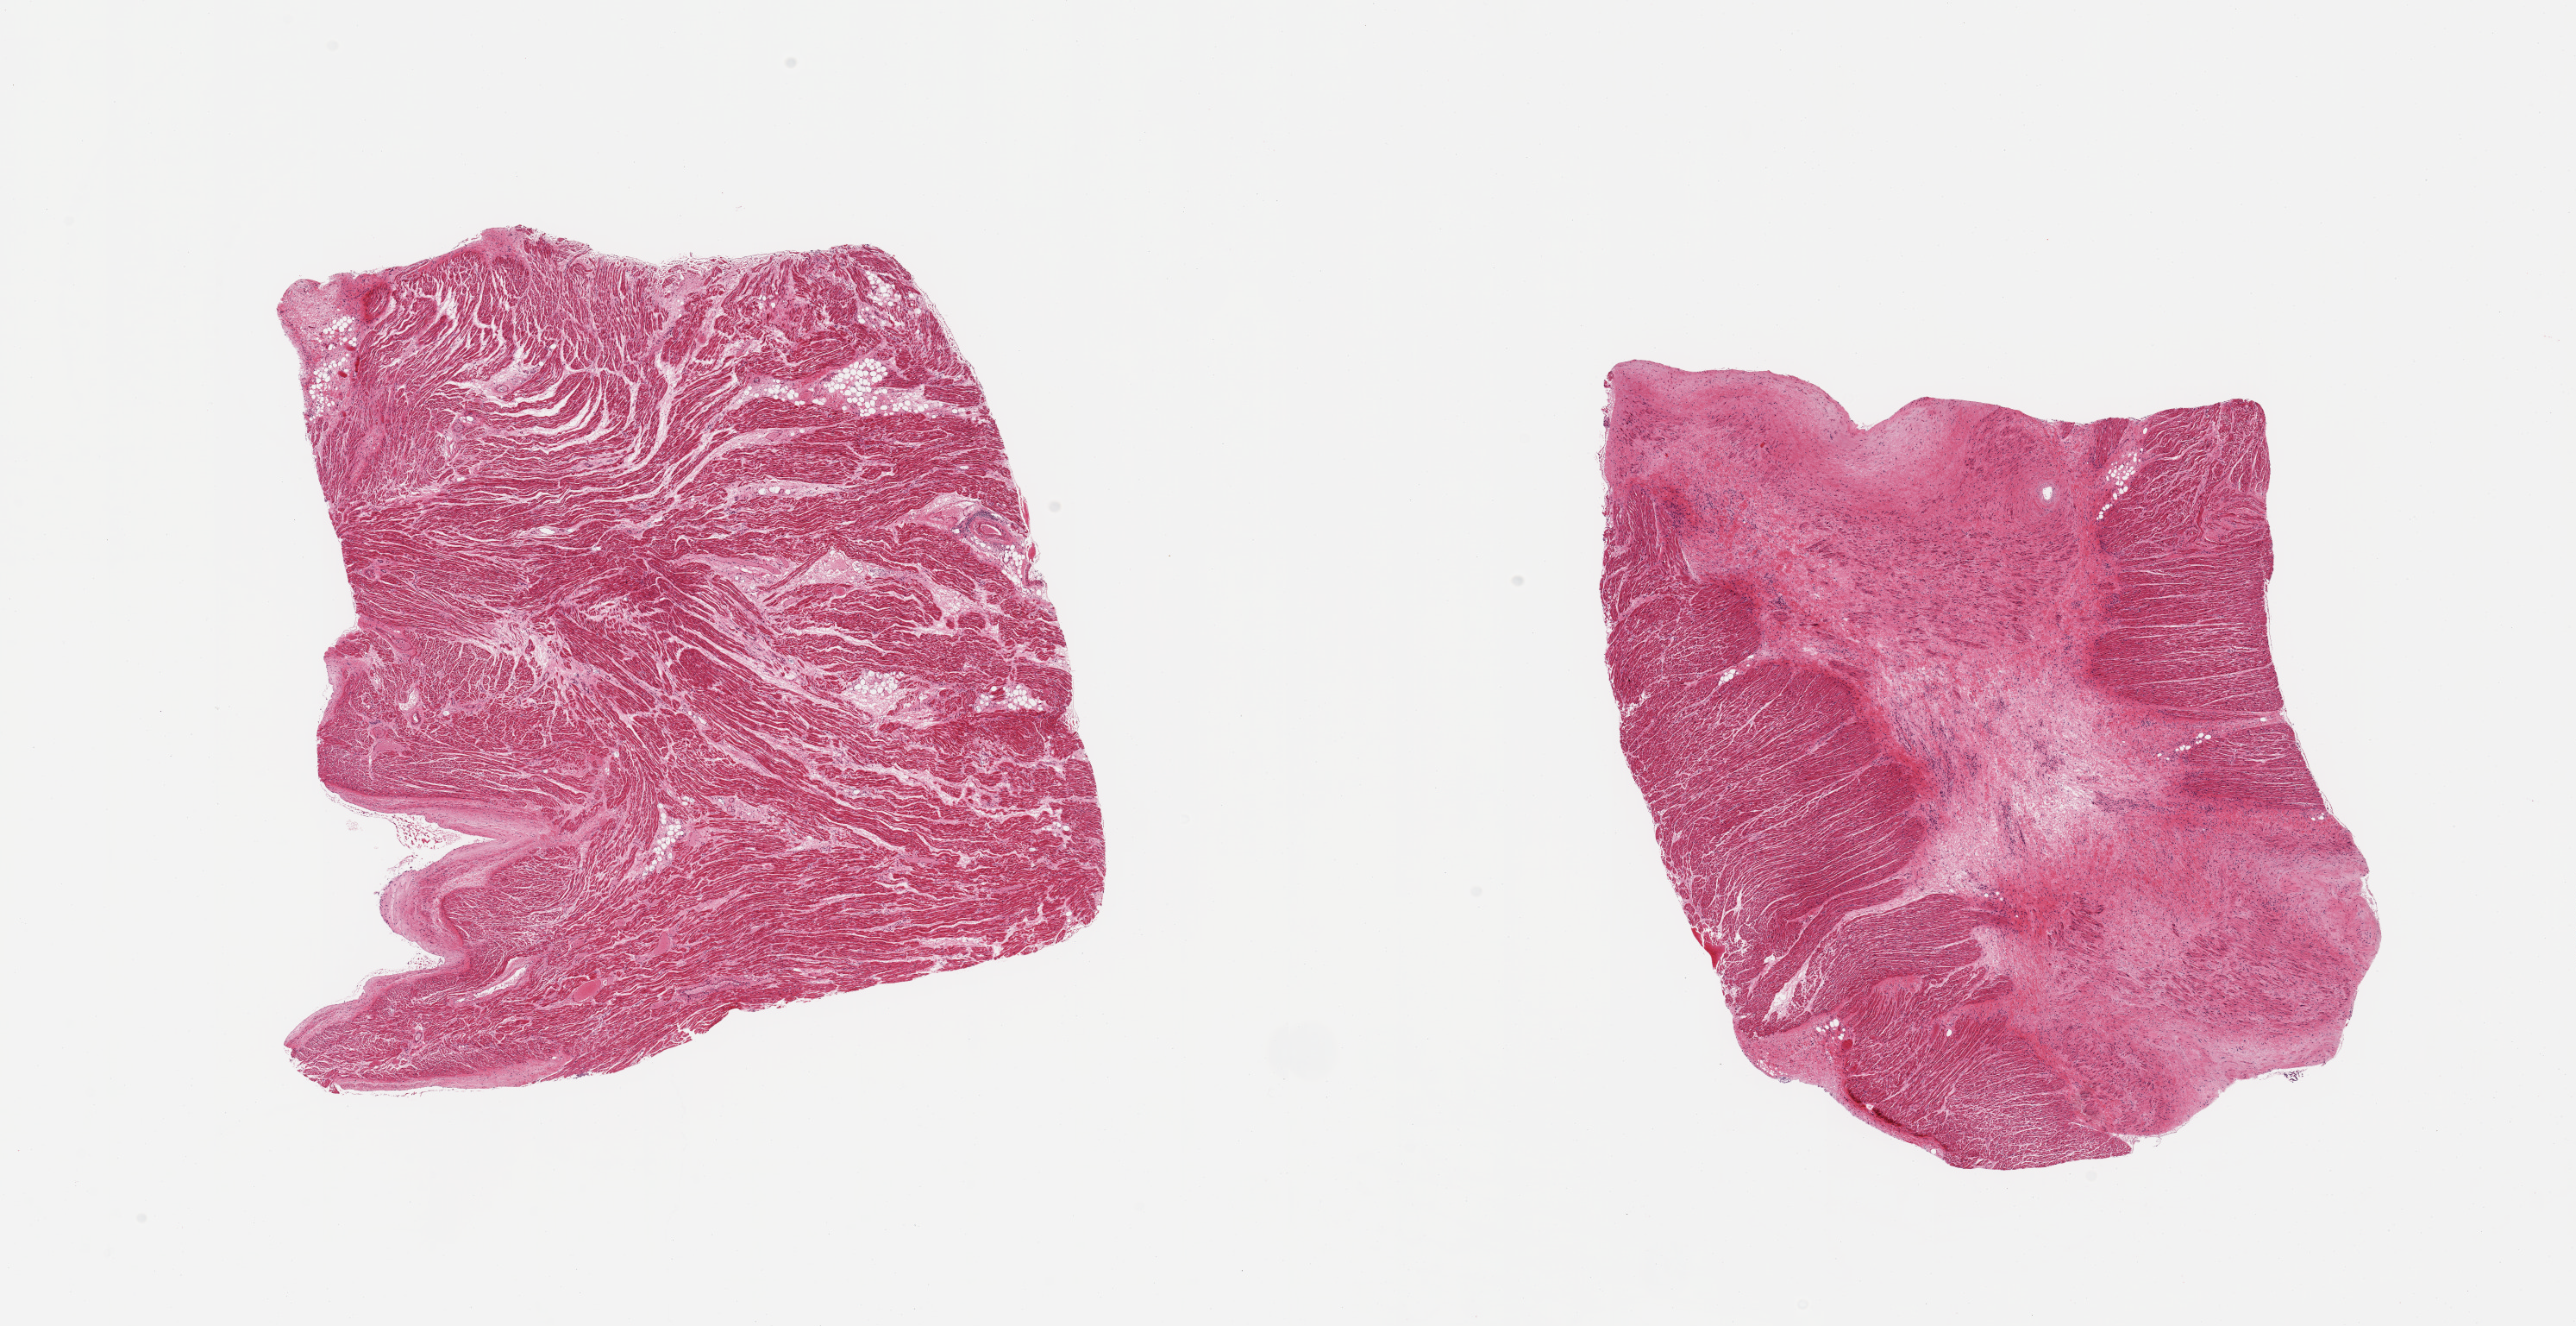
Whole-slide image, hematoxylin and eosin (H&E) stain, whole scanned area (about 23.6 x 12.2 mm, slide scanned at 20x) shown as a low-resolution overview, PAXgene-fixed, paraffin-embedded tissue, section of auricular appendage (target tissue), tissue donor sample. Donor sex: female.
Review note (as recorded): 2 pieces; one piece is ~50% fibrous.